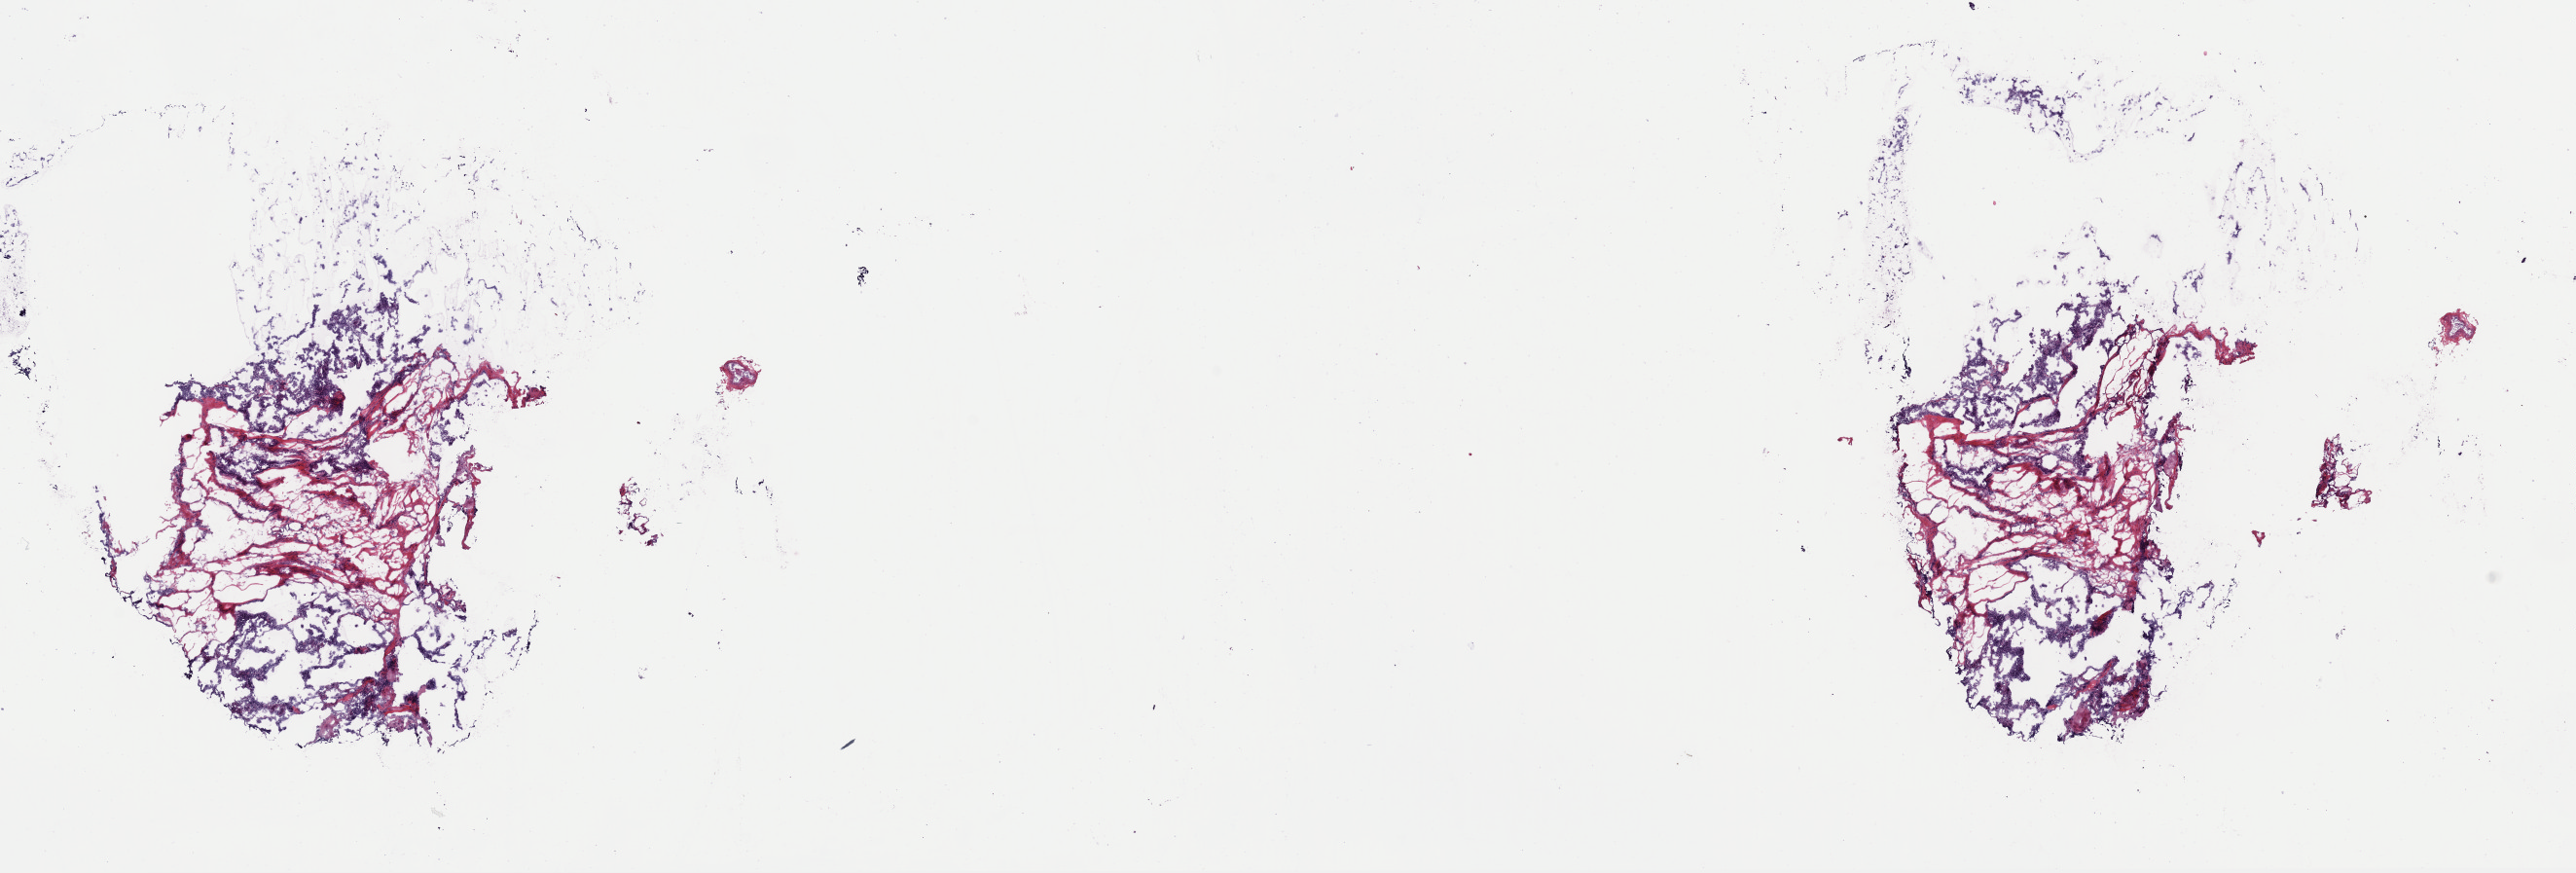
Hematoxylin and eosin (H&E) stained whole-slide image — whole scanned area (about 20.9 x 7.1 mm, from a 40x scan) shown as a low-resolution overview, frozen section from the top of the tissue portion, sample: primary tumour, thyroid. Female patient; age at initial diagnosis 54 years. Slide review estimates, as recorded: tumour cells 60%, tumour nuclei 65%, normal cells 0%, stromal cells 40%, necrosis 0%. Inflammatory infiltration, as recorded: lymphocyte infiltration 2%, monocyte infiltration 1%, neutrophil infiltration 0%.
- lymph nodes positive (case pathology): 0 of 1 examined
- AJCC pathologic stage: I (7th edition)
- histologic diagnosis: Papillary adenocarcinoma, NOS (thyroid gland)